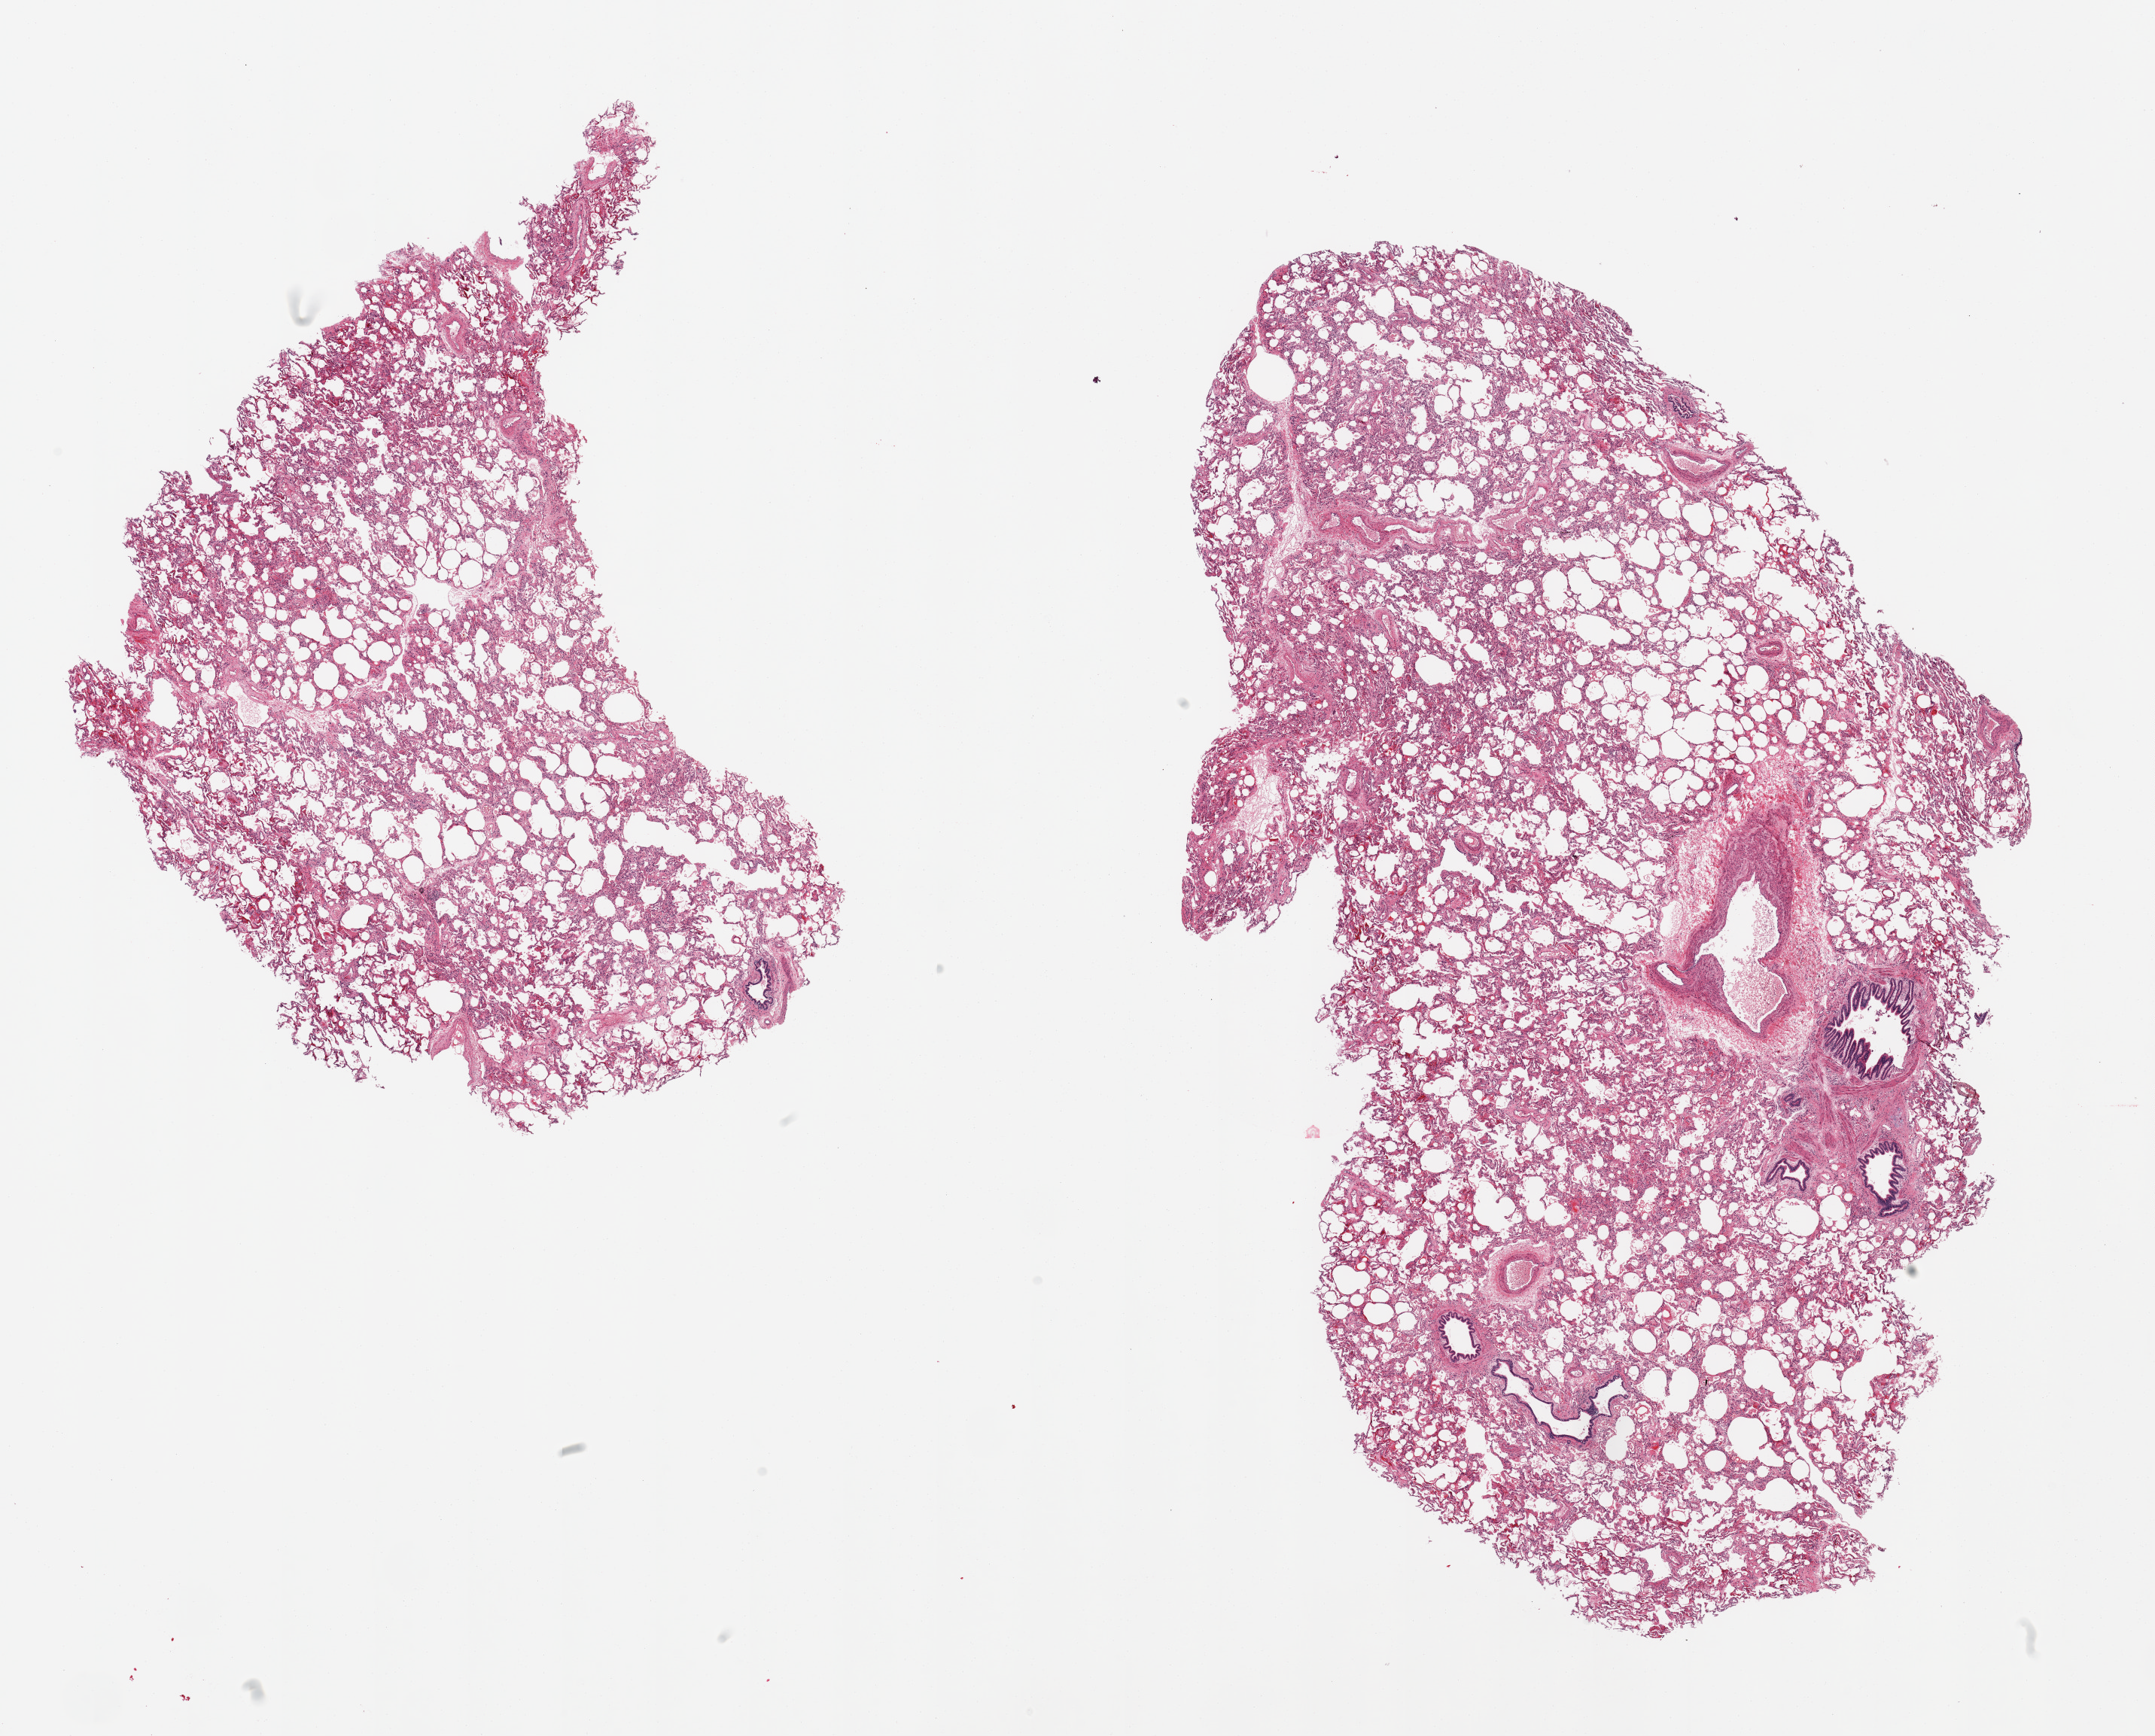
Digitized haematoxylin and eosin-stained section, whole scanned area (about 22.6 x 18.2 mm) shown as a low-resolution overview; PAXgene-fixed paraffin-embedded (PFPE) section; target tissue: lung; tissue donor sample. Donor: female.
• review note (as recorded): 2 pieces, mild congestion, foci of well-preserved bronchial mucosa